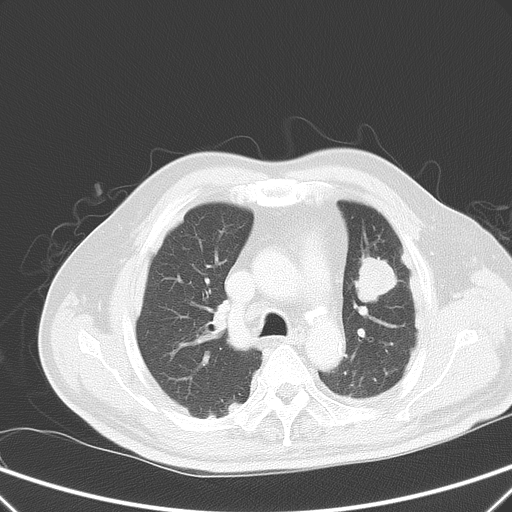
Chest CT, one axial slice; position 41 of 59 along the scan axis; 120 kVp; lung window (W 1500 / L -600 HU); 5 mm slice thickness; 512 × 512 image matrix, field of view 357 × 357 mm. Male patient, age 66 years. From the clinical record (not read from this slice): clinical TNM (as recorded): T1c N3 M1a.
Structures marked on this image (bounding box drawn by a radiologist):
- lung tumour (recorded histology: squamous cell carcinoma): bounding box [x1, y1, x2, y2] px = [351, 252, 405, 311]